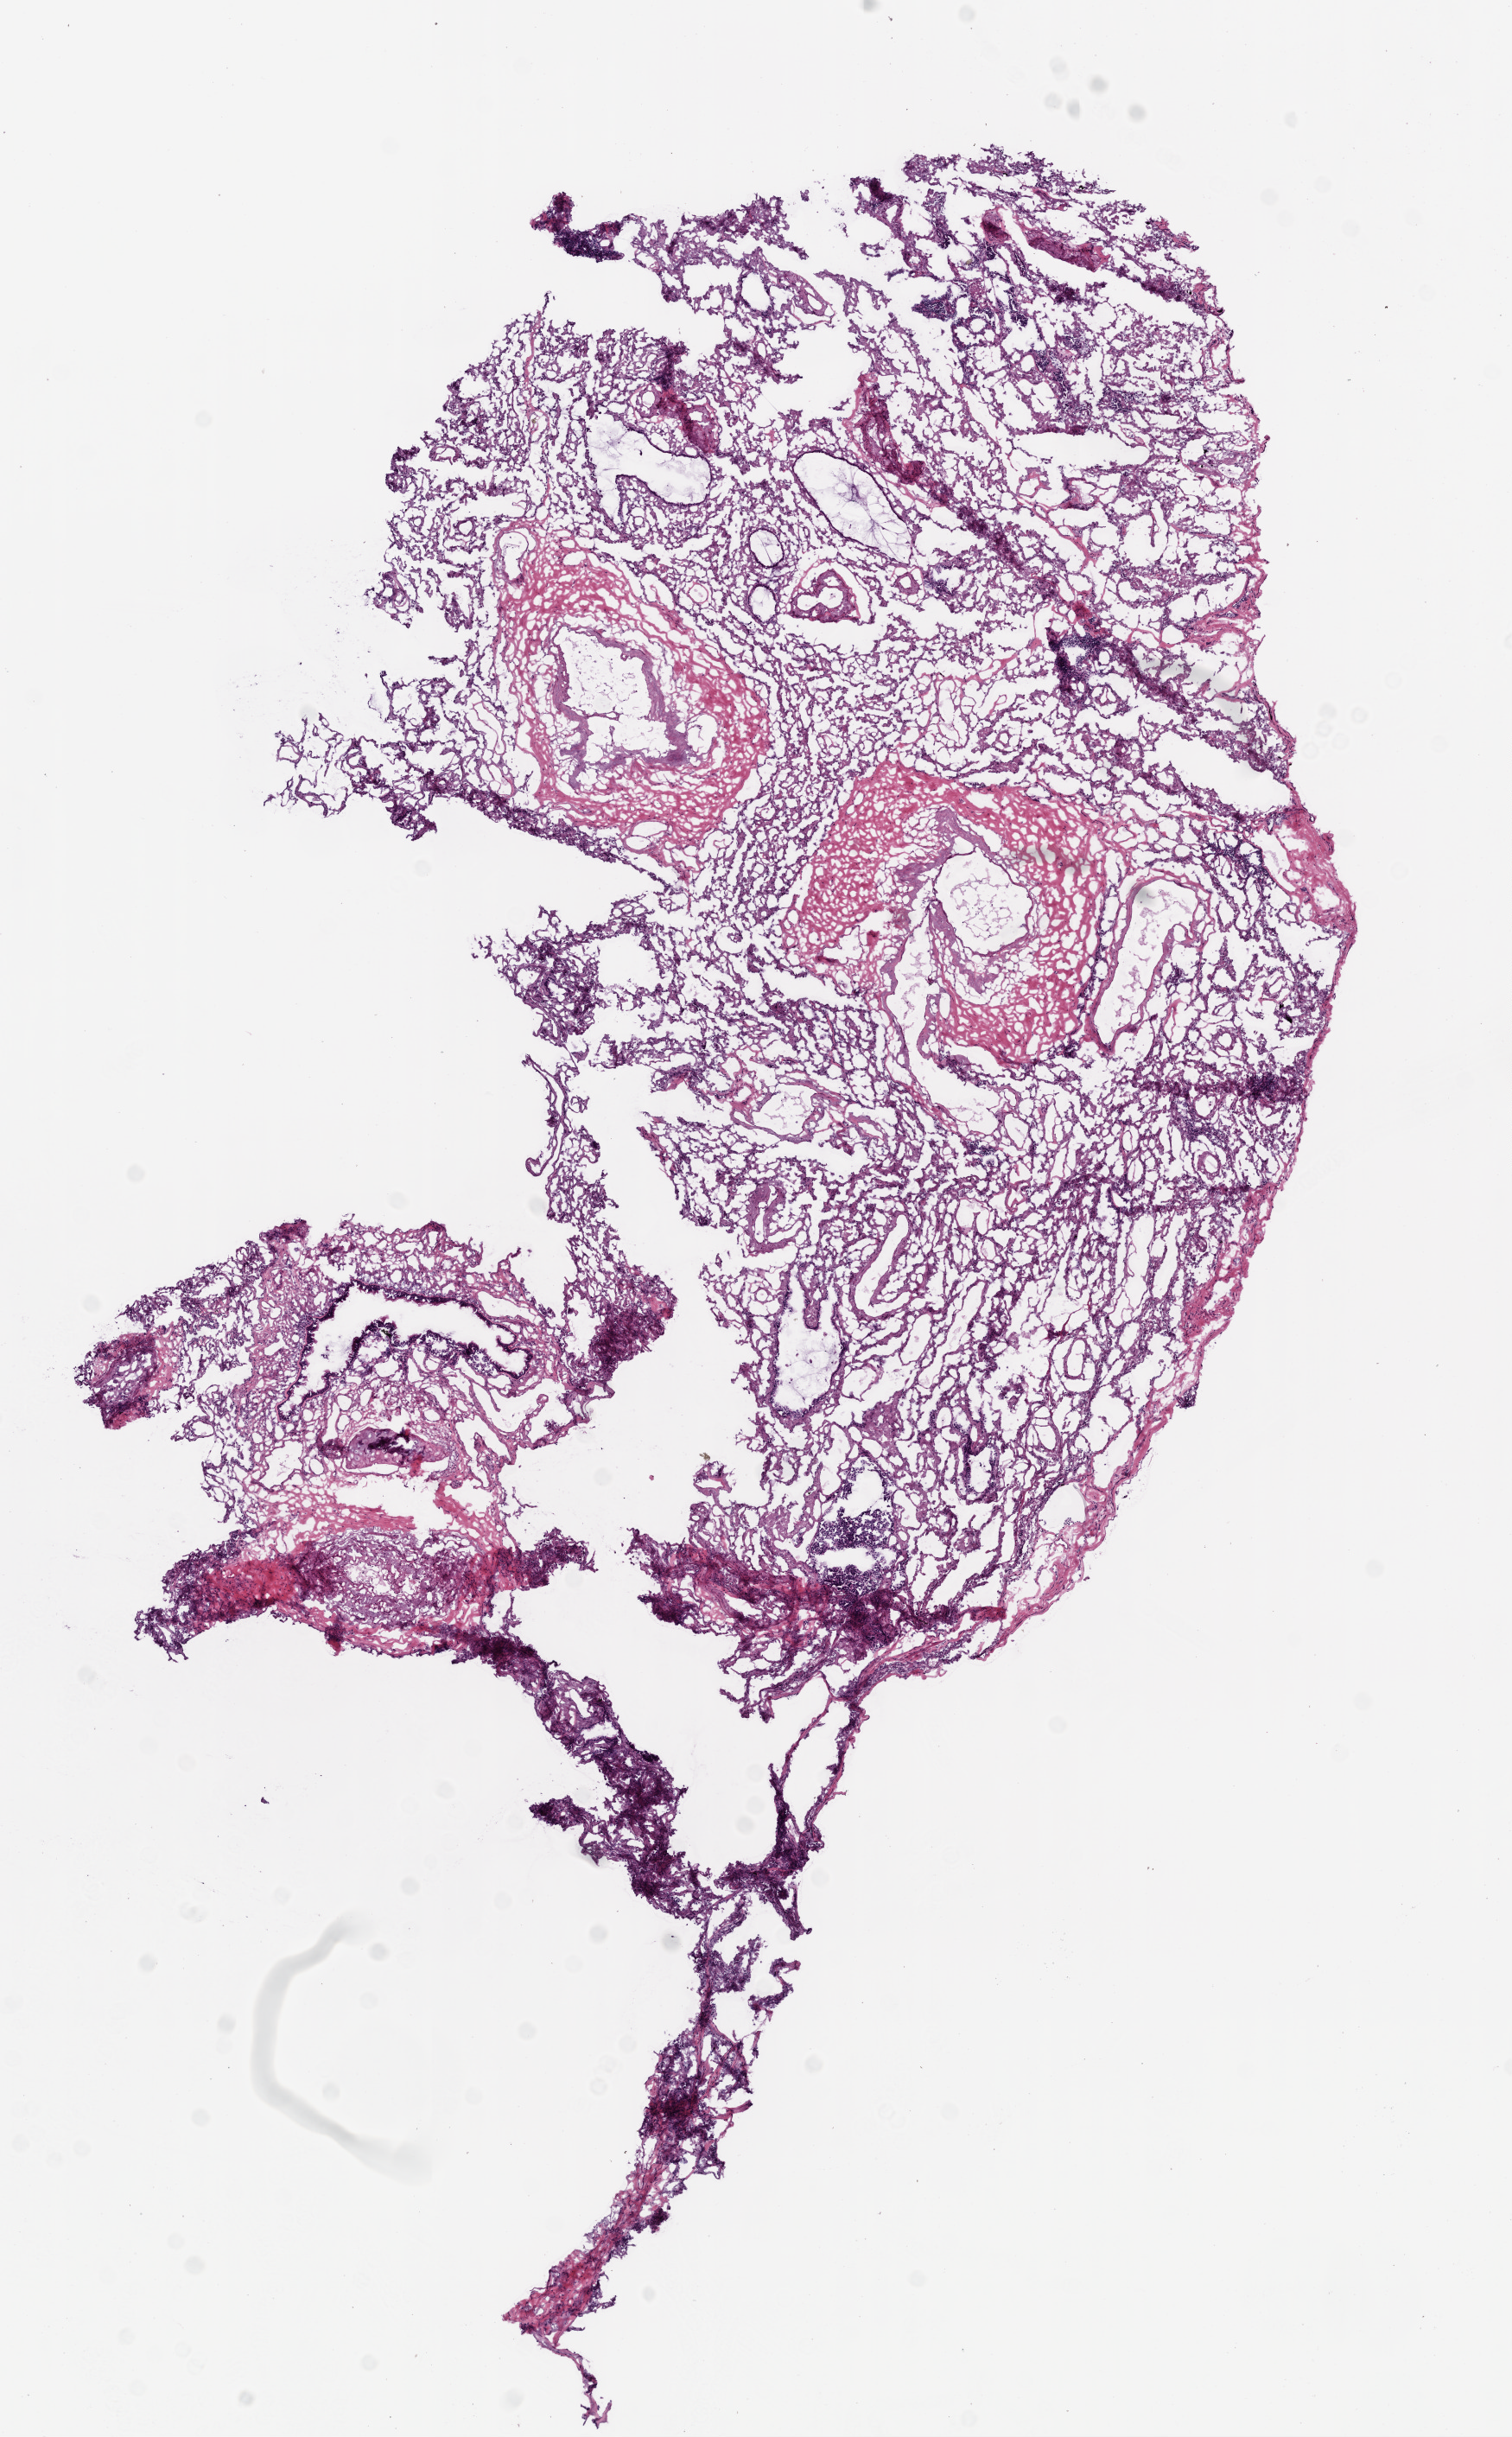
Hematoxylin and eosin (H&E) stained whole-slide image — a low-resolution overview of the entire scanned area, about 7.0 x 11.3 mm (slide scanned at 20x); frozen section; solid tissue normal (non-tumour tissue) sample from the lung. Patient: female, age at initial diagnosis 79 years.
This section: solid tissue normal (non-tumour) sample from the same patient. Patient diagnosis: Papillary adenocarcinoma, NOS (upper lobe, lung).